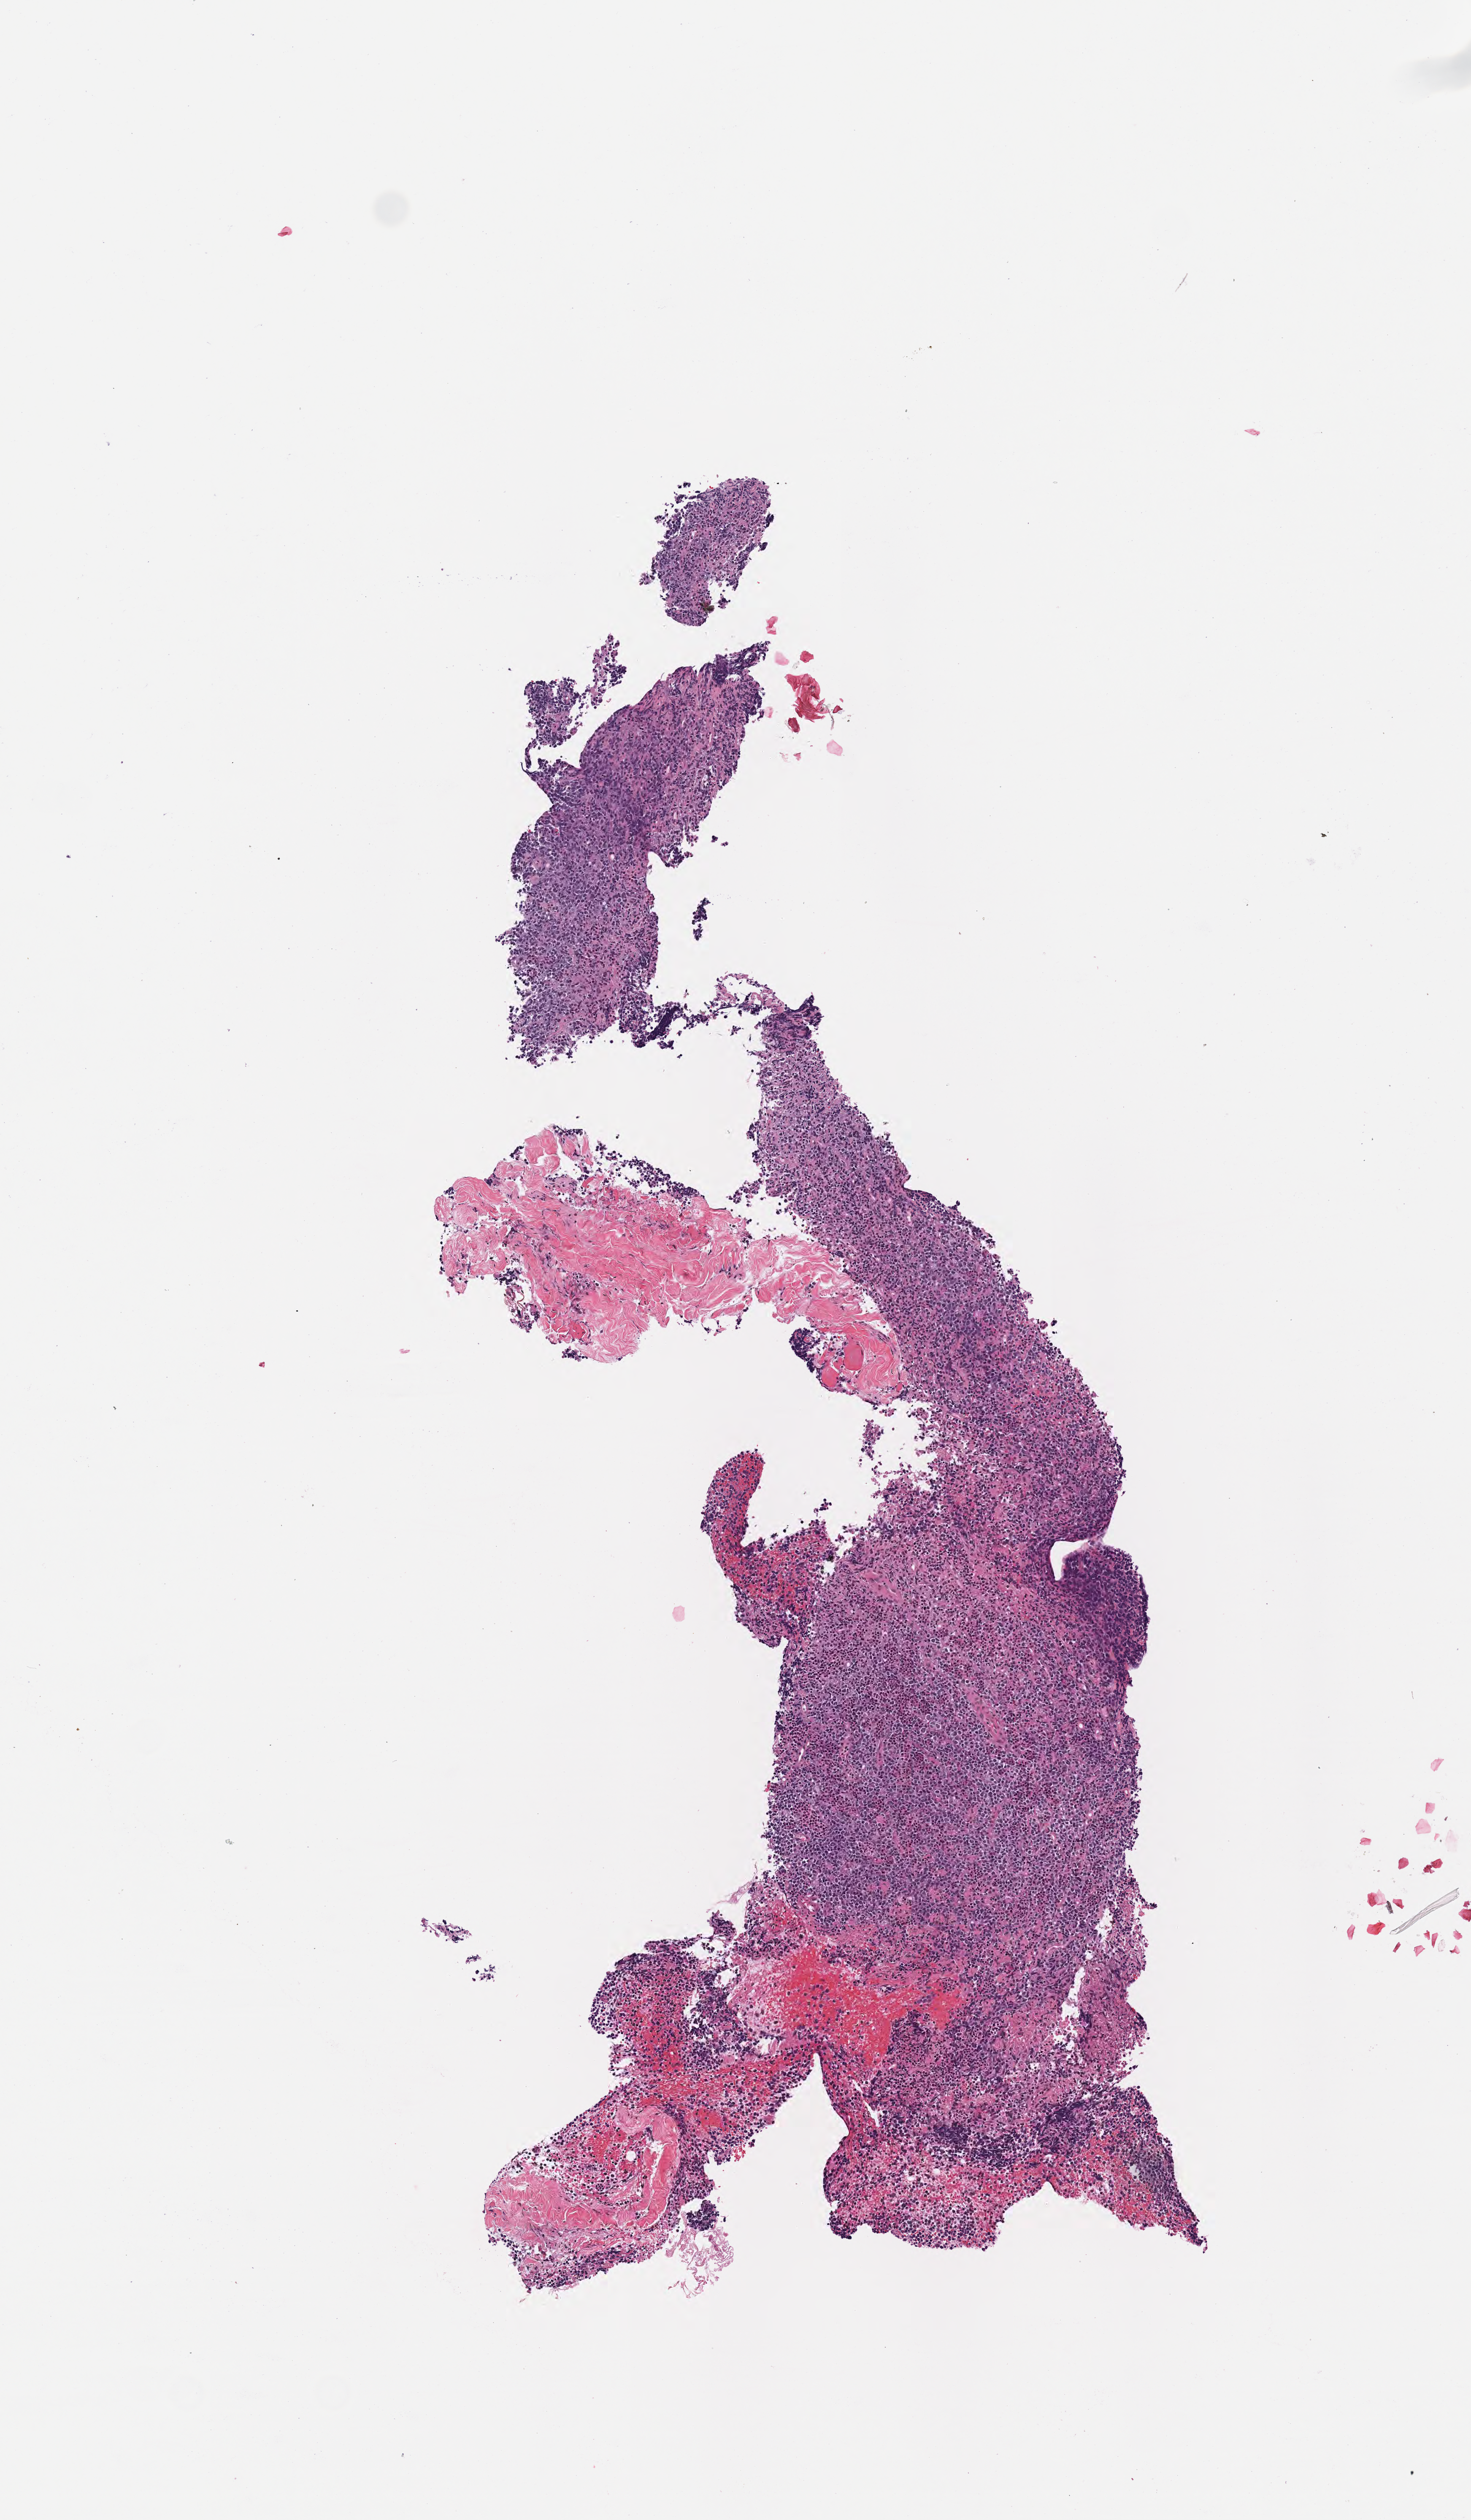
Digitized haematoxylin and eosin-stained section, low-resolution overview of the scanned area, about 3.5 x 6.0 mm. Specimen: tumor tissue. Patient: female, age 27 years.
* histologic diagnosis: Diffuse large B-cell lymphoma, NOS